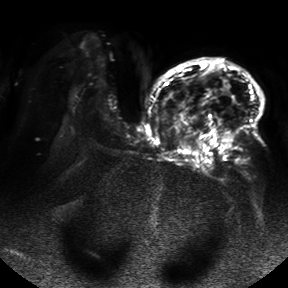
Breast MRI, one axial slice; diffusion-weighted series; image 2 of 4 stored at this slice position (different b-values; order by instance number); 1.5 T; 4 mm slice thickness; 288 × 288 image matrix. Female patient.
Outlined on this slice (expert manual segmentation):
- tumour on diffusion-weighted imaging: bounding box [x1, y1, x2, y2] px = [223, 131, 234, 148]